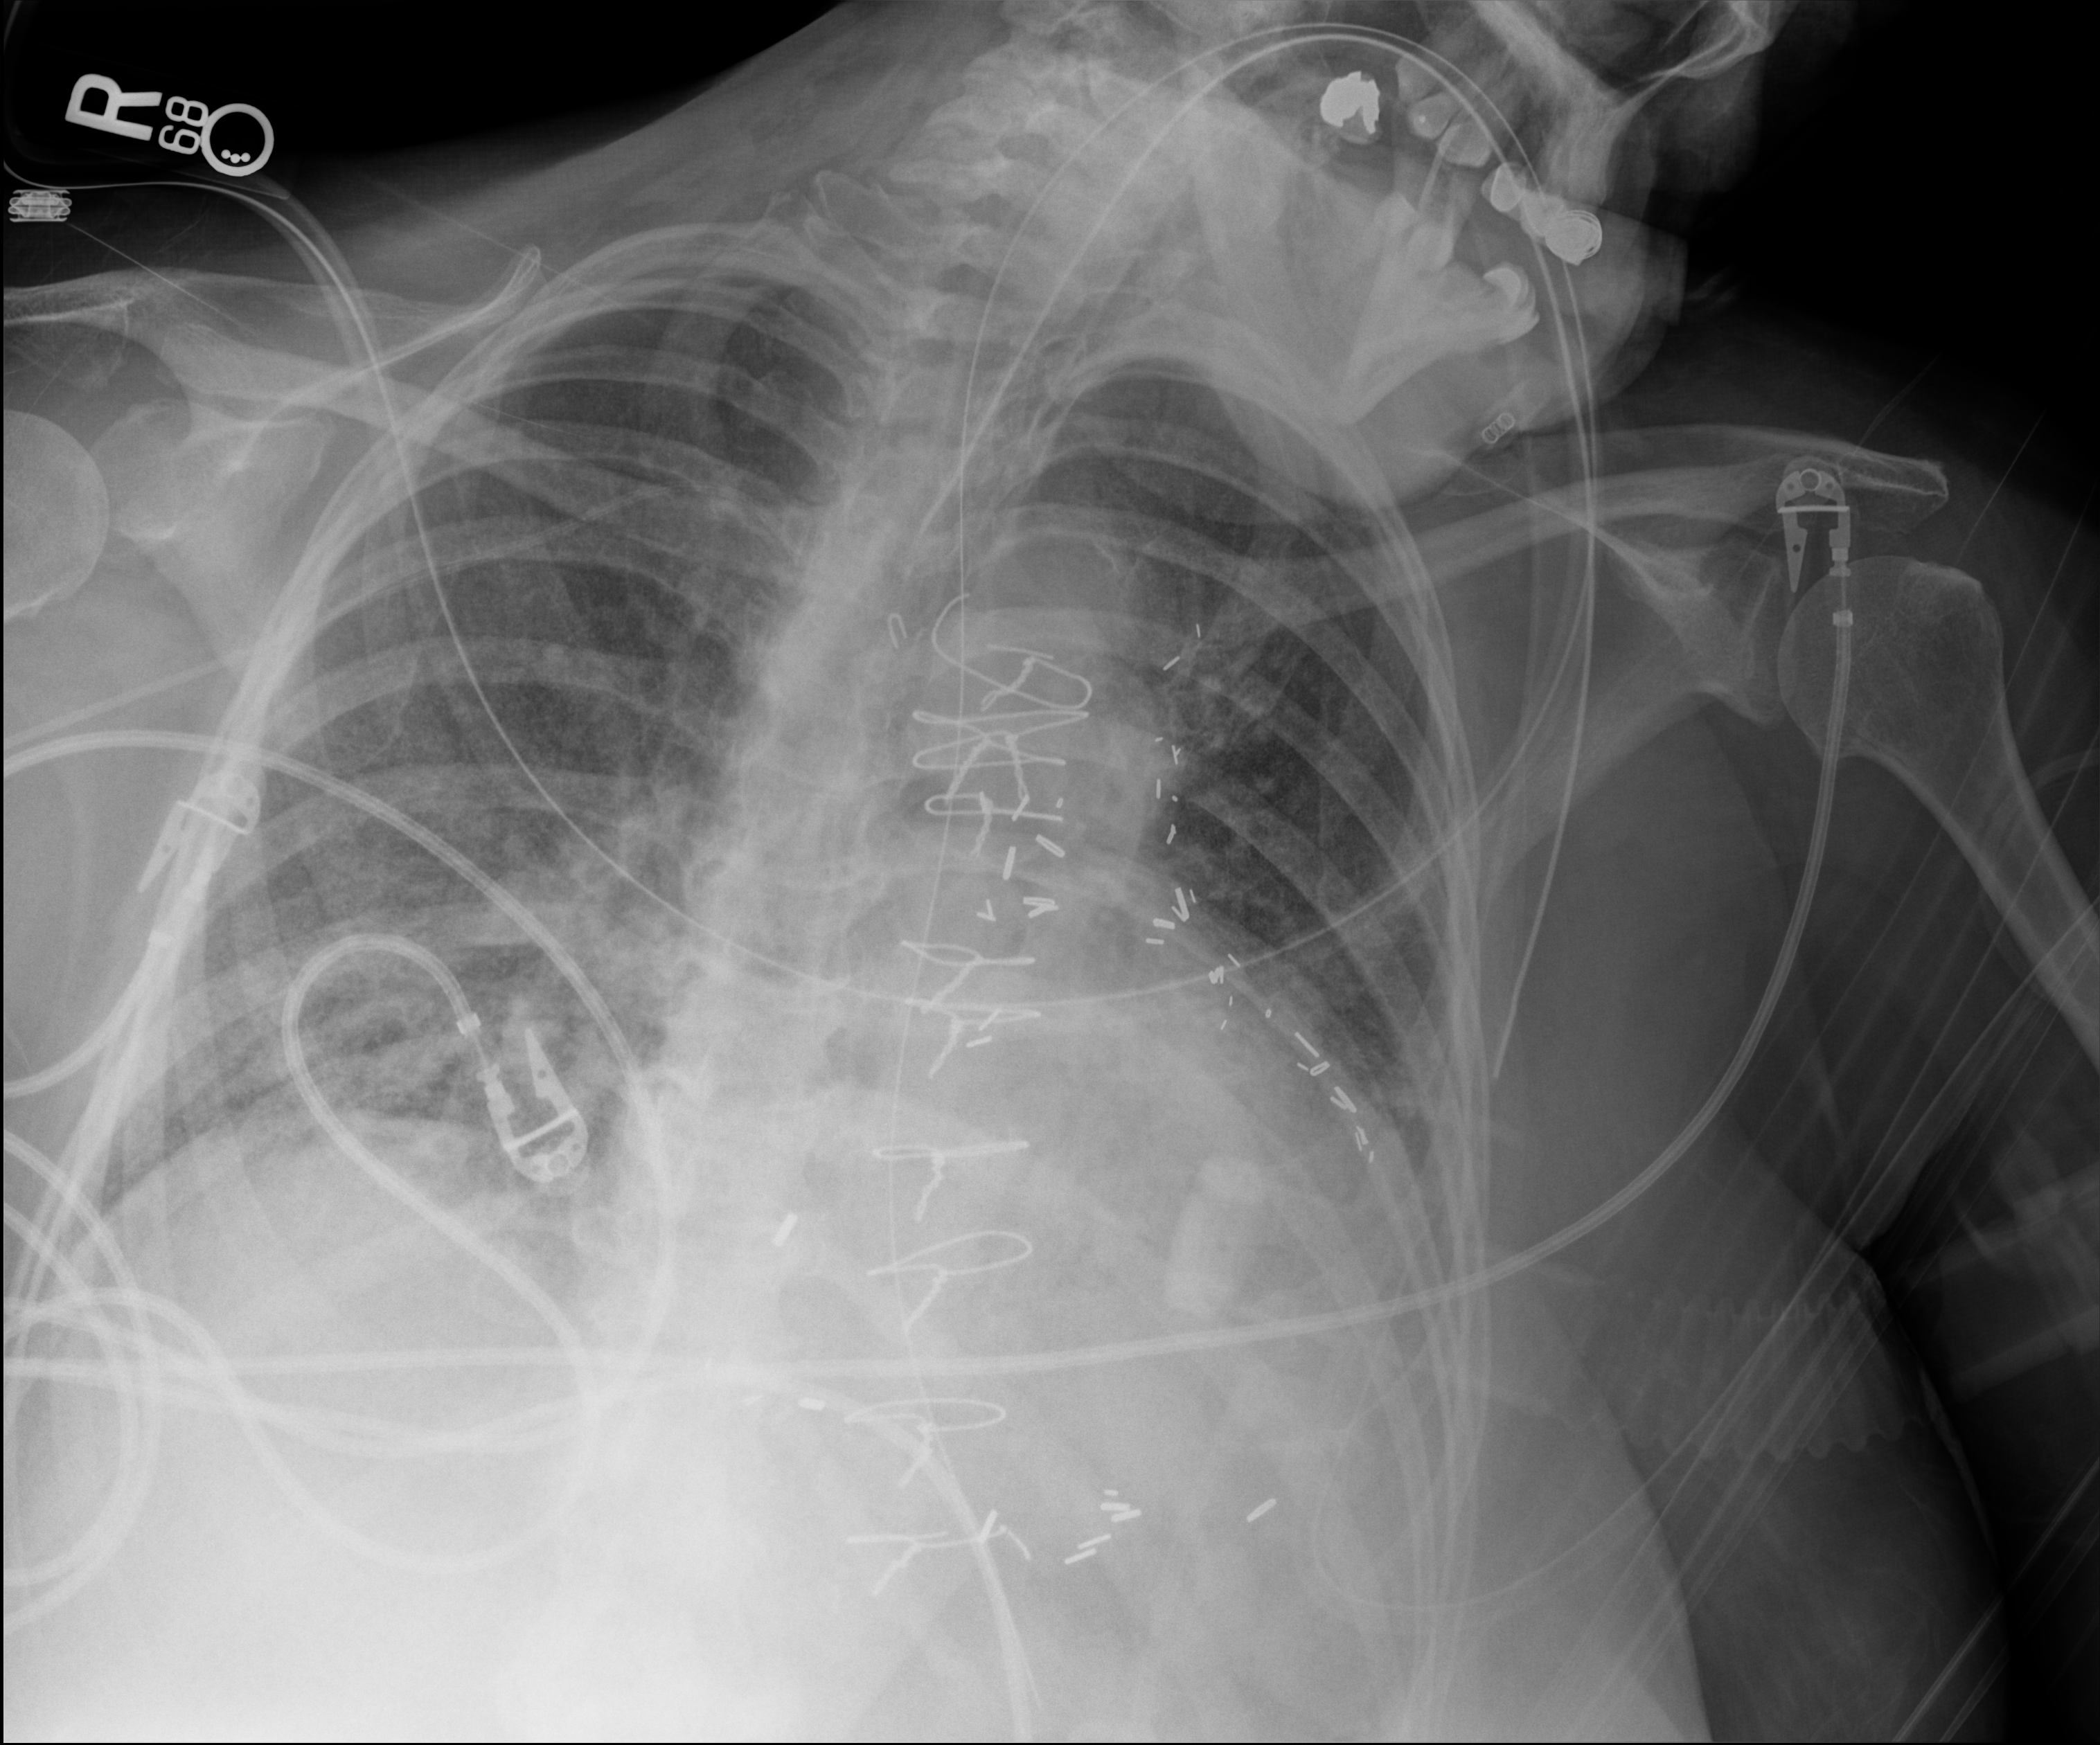
Portable chest radiograph; anteroposterior (AP) projection. Patient hospitalised with COVID-19; female, aged 60–74 years.
From the hospital-stay record, not from the radiograph (when in the stay this image was taken is not recorded): admitted to intensive care during this hospital stay: yes; smoking status (admission record): never.